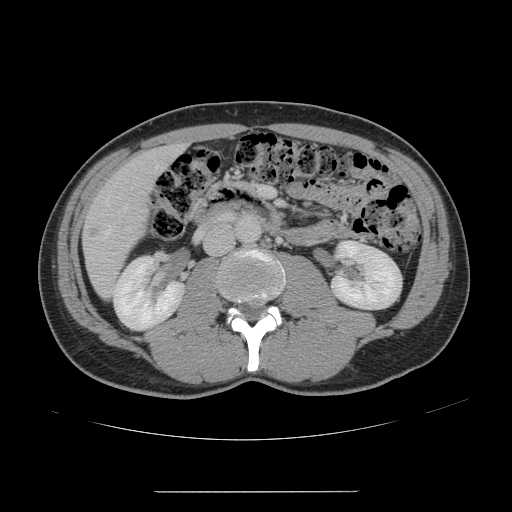
Contrast-enhanced abdominal CT, one axial slice; position 50 of 178 along the scan axis; 120 kVp; intravenous contrast given; soft-tissue window (W 400 / L 40 HU); 2.5 mm slice thickness; 512 × 512 image matrix, field of view 401 × 401 mm. Male patient, age 53 years. Case-level facts recorded for this patient, not image findings: diagnosis: colorectal cancer liver metastases, imaged before liver resection; multiple liver metastases: yes; largest metastasis: 2.4 cm; disease in both lobes: no.
Annotated regions visible in this slice (outlined manually by an expert reader):
- hepatic veins: bounding box [x1, y1, x2, y2] px = [101, 166, 158, 240]
- liver: [84, 147, 179, 296]
- portal vein (with intrahepatic branches): [259, 186, 267, 195]
- liver metastasis: [88, 228, 96, 238]